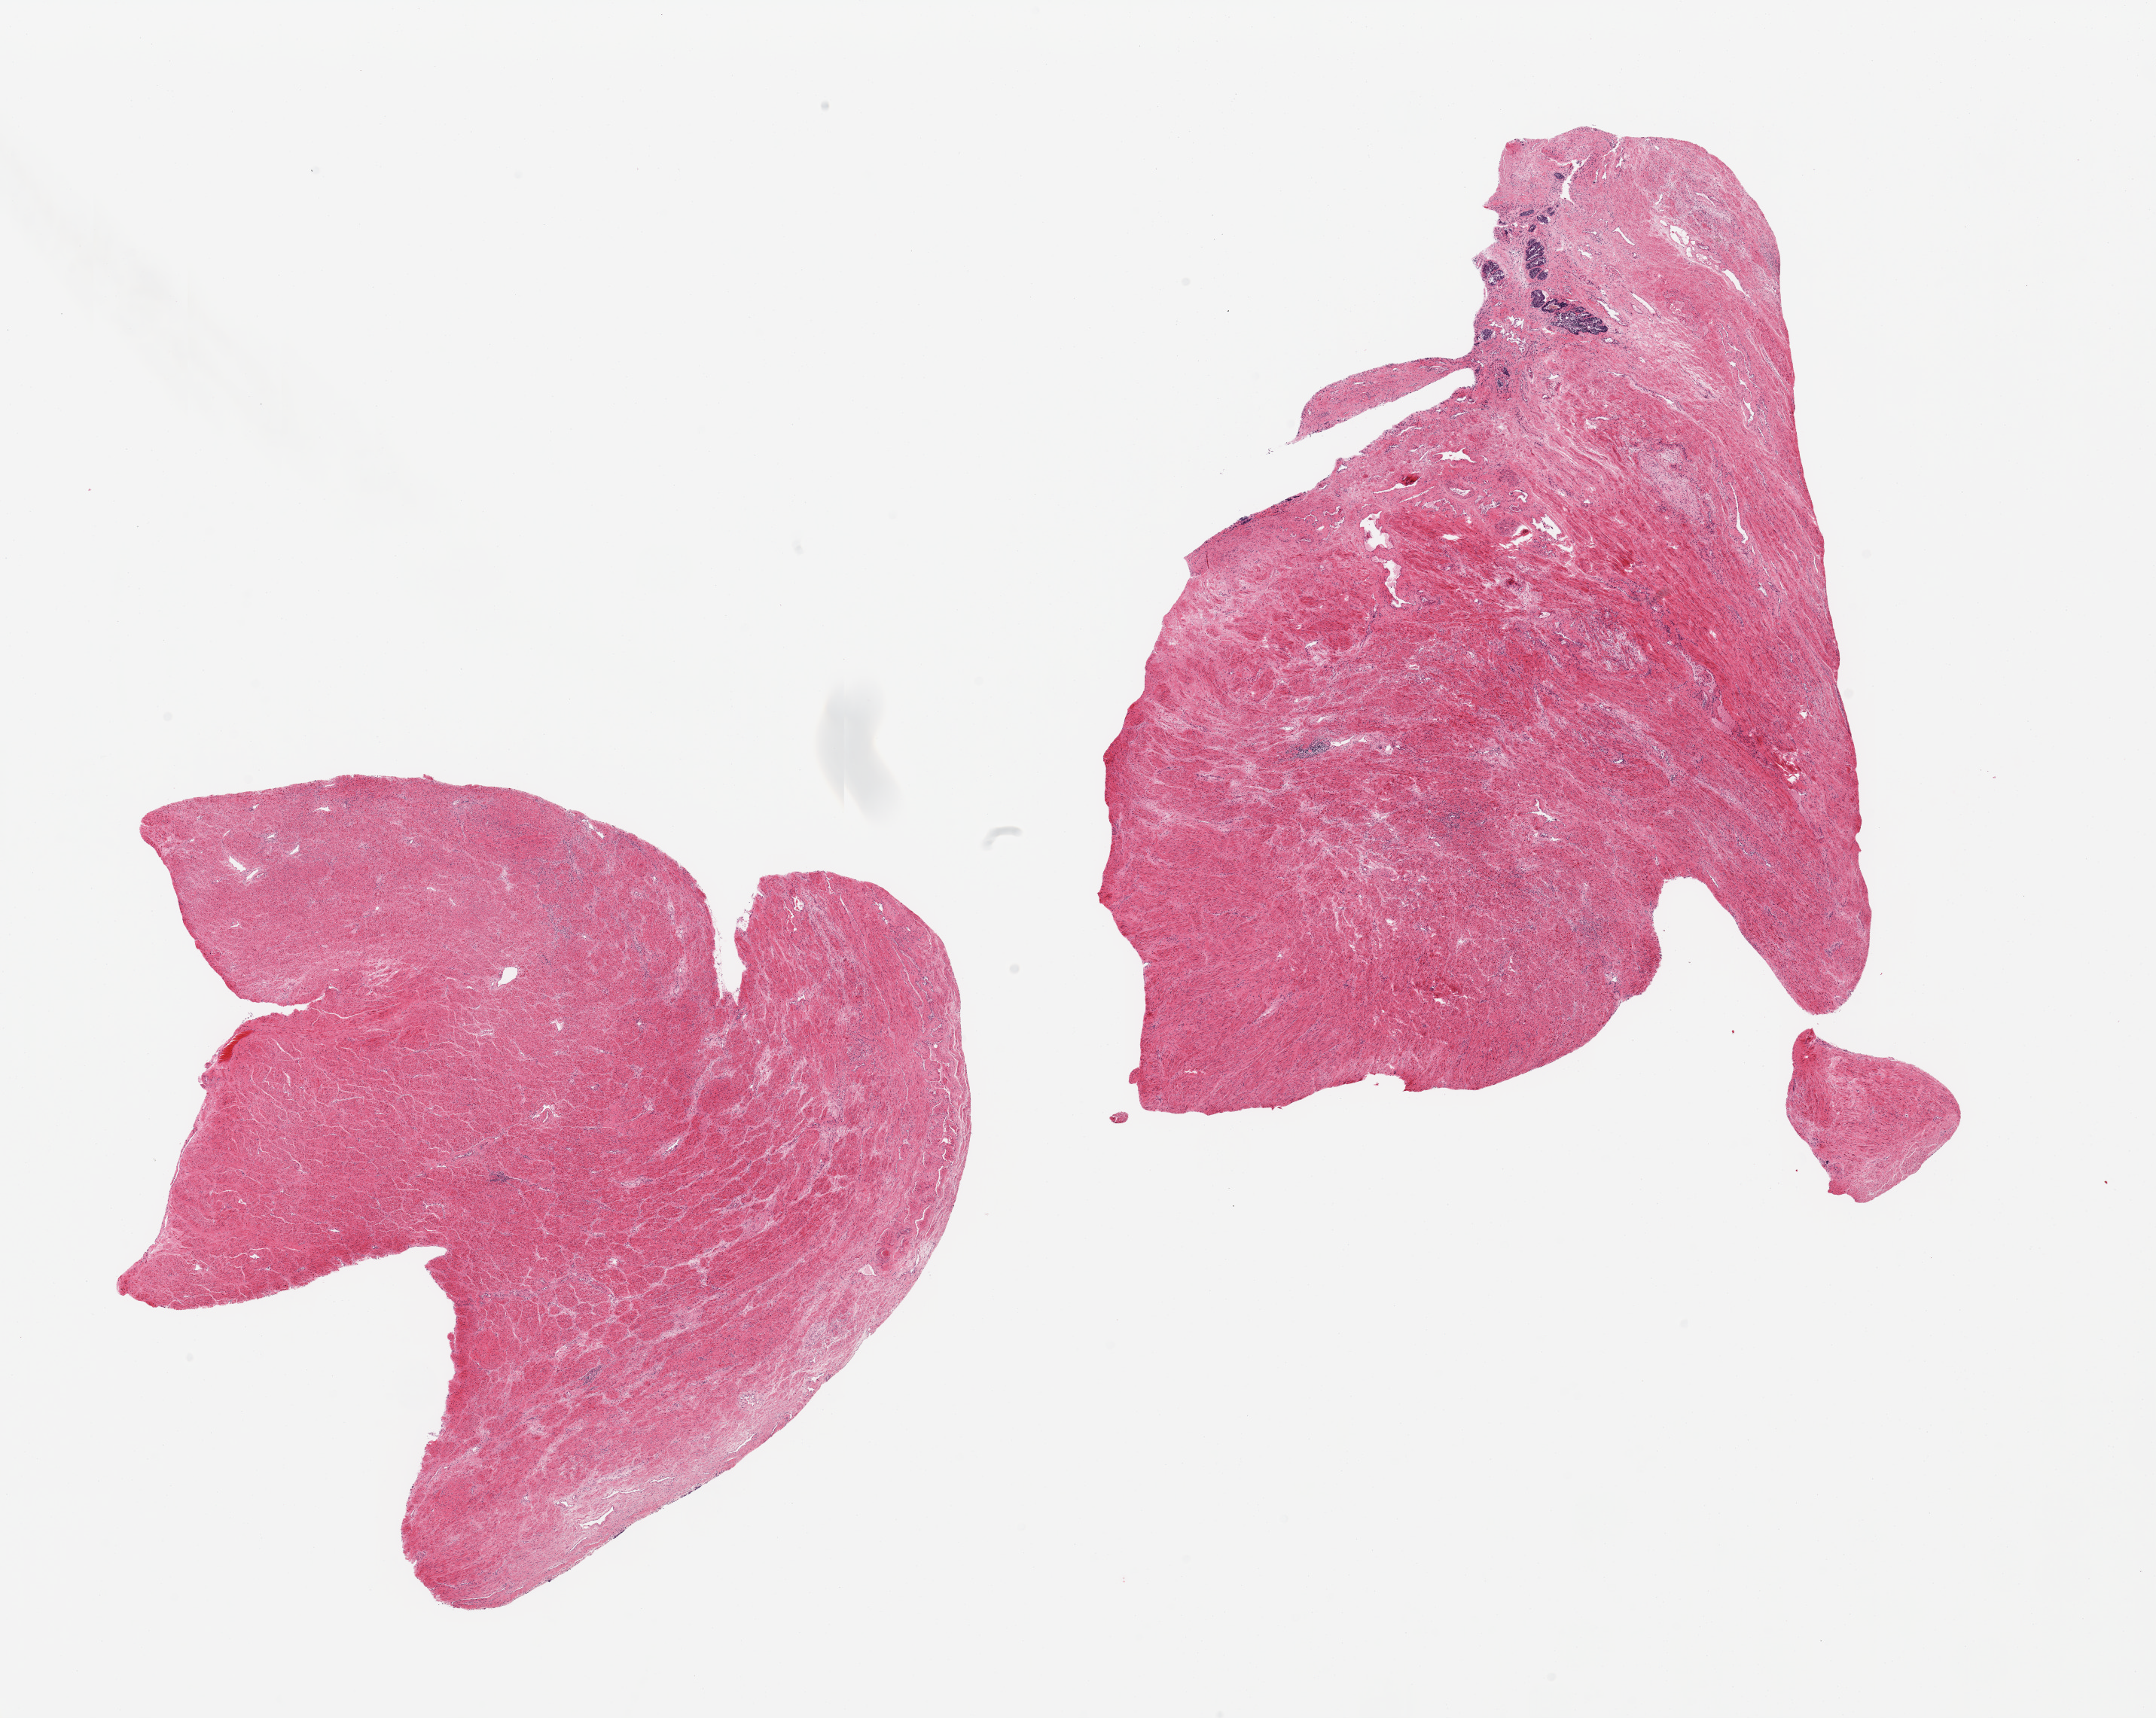
Haematoxylin and eosin whole-slide image, brightfield, shown as a low-resolution overview of the whole scanned area (about 22.6 x 18.0 mm, from a 20x scan); PAXgene-fixed, paraffin-embedded tissue; target tissue: prostate; donor tissue sample. Donor sex: male.
Review note (as recorded): 2 pieces; predominantly stromal hyperplasia with only small glandular focus.